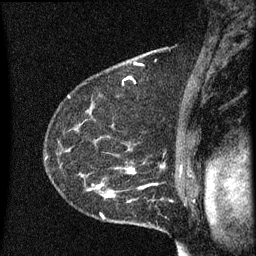
Breast MRI (dynamic contrast-enhanced), one sagittal slice; slice 44 of 60 in the series (ordered by position); dynamic contrast-enhanced series, image 2 of 3 at this slice position (ordered by acquisition); 1.5 T; TE 4.2 ms, TR 8 ms; 2 mm slice thickness; 256 × 256 image matrix, field of view 180 × 180 mm. Female patient, age 55 years.
Annotated regions visible in this slice (semi-automatically segmented with operator editing):
- analysis volume of interest (the breast-tissue region the enhancement analysis was run in; not a lesion): bounding box <51,156,145,217> (left, top, right, bottom; pixels)
- tumour enhancement mask (voxels above the 70 % enhancement threshold inside the analysis volume of interest): <87,166,145,217>